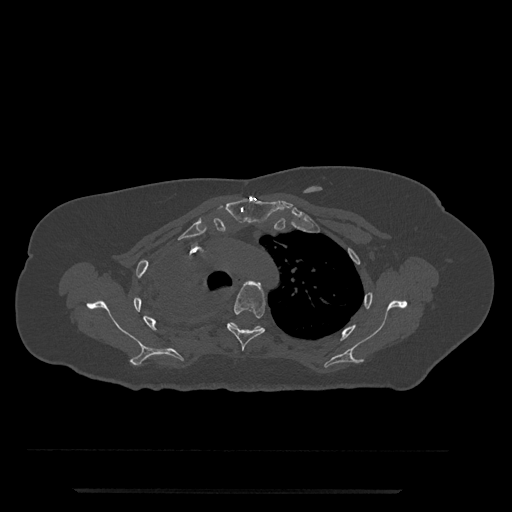
CT including the spine, one axial slice; position 585 of 797 along the scan axis; reconstruction kernel Br40s/3; 120 kVp; bone window (W 1800 / L 400 HU); 512 × 512 image matrix. Patient: female, 51 years. Case-level facts recorded for this patient, not image findings: primary cancer: neuro.
Structures marked on this image (semi-automatic segmentation, software-assisted and operator-edited):
- T3 vertebra: bounding box (x1, y1, x2, y2) in pixels: (246, 282, 261, 285)
- T4 vertebra: (227, 282, 266, 351)
- T5 vertebra: (229, 322, 263, 331)